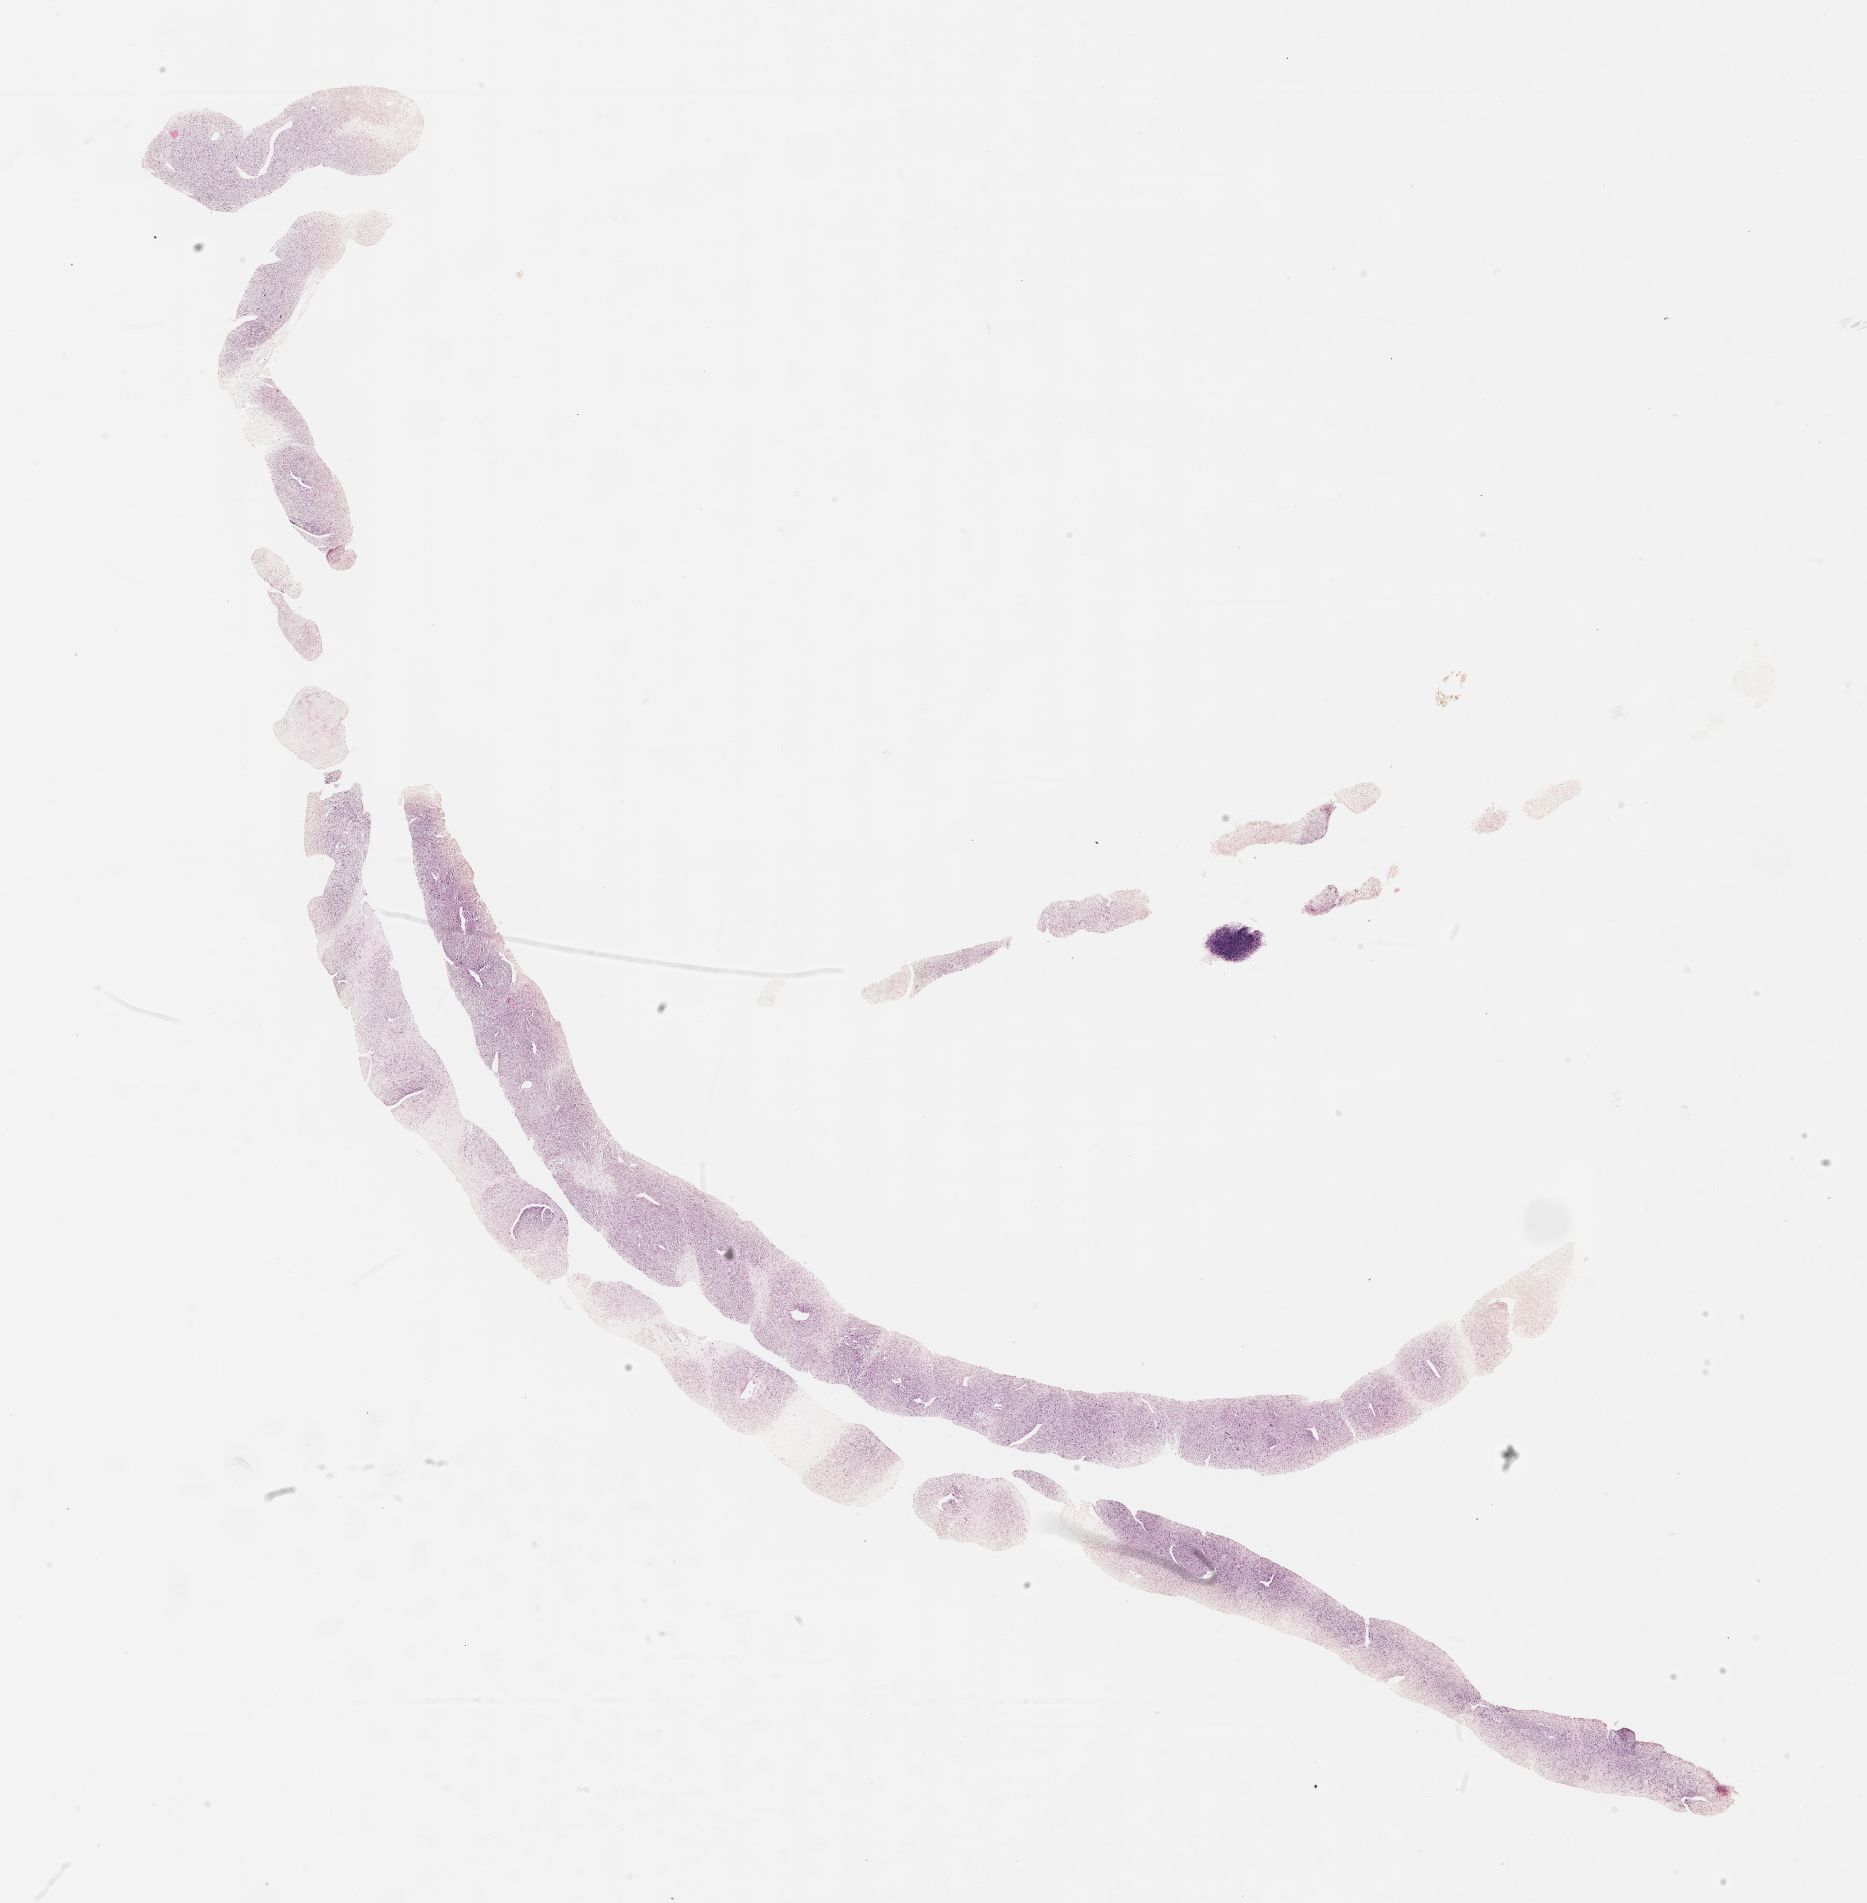
Whole-slide image, haematoxylin and eosin stain of tumor tissue, whole scanned area (about 15.1 x 15.4 mm) shown as a low-resolution overview. Formalin-fixed, paraffin-embedded (FFPE) tissue. Sample anatomic site: soft tissue, armpit-right. Patient: male, age 2.8 years at diagnosis.
- diagnosis: rhabdomyosarcoma; histological classification: embryonal rhabdomyosarcoma
- metastatic status at presentation (as recorded): non-metastatic
- stage (as recorded): 3